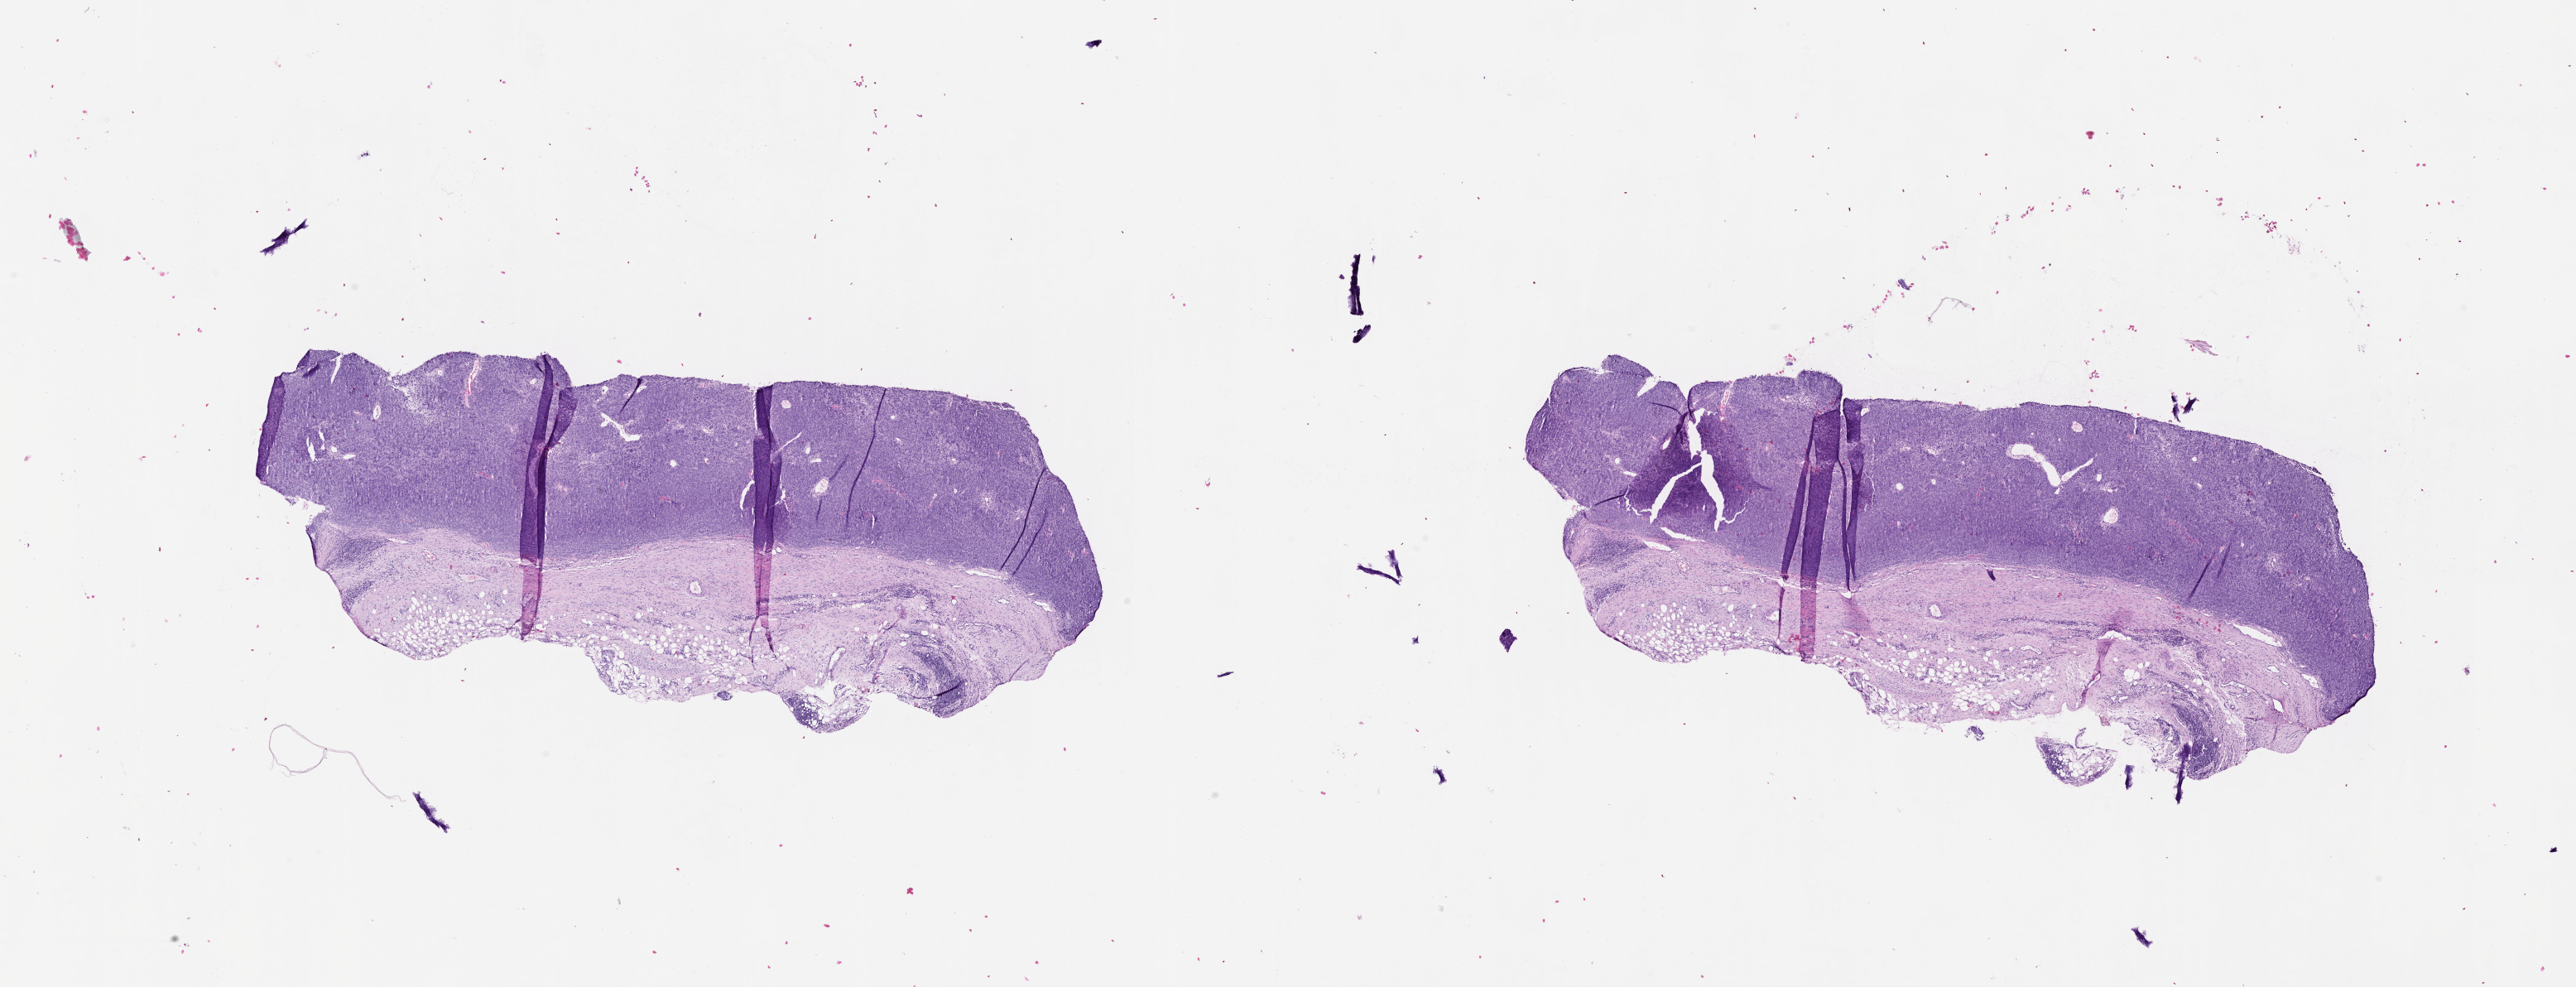
H&E whole-slide image, low-resolution overview of the scanned area, about 25.1 x 9.6 mm (slide scanned at 20x). Patient: male, age 72 years.
Patient diagnosis: Malignant melanoma, NOS.